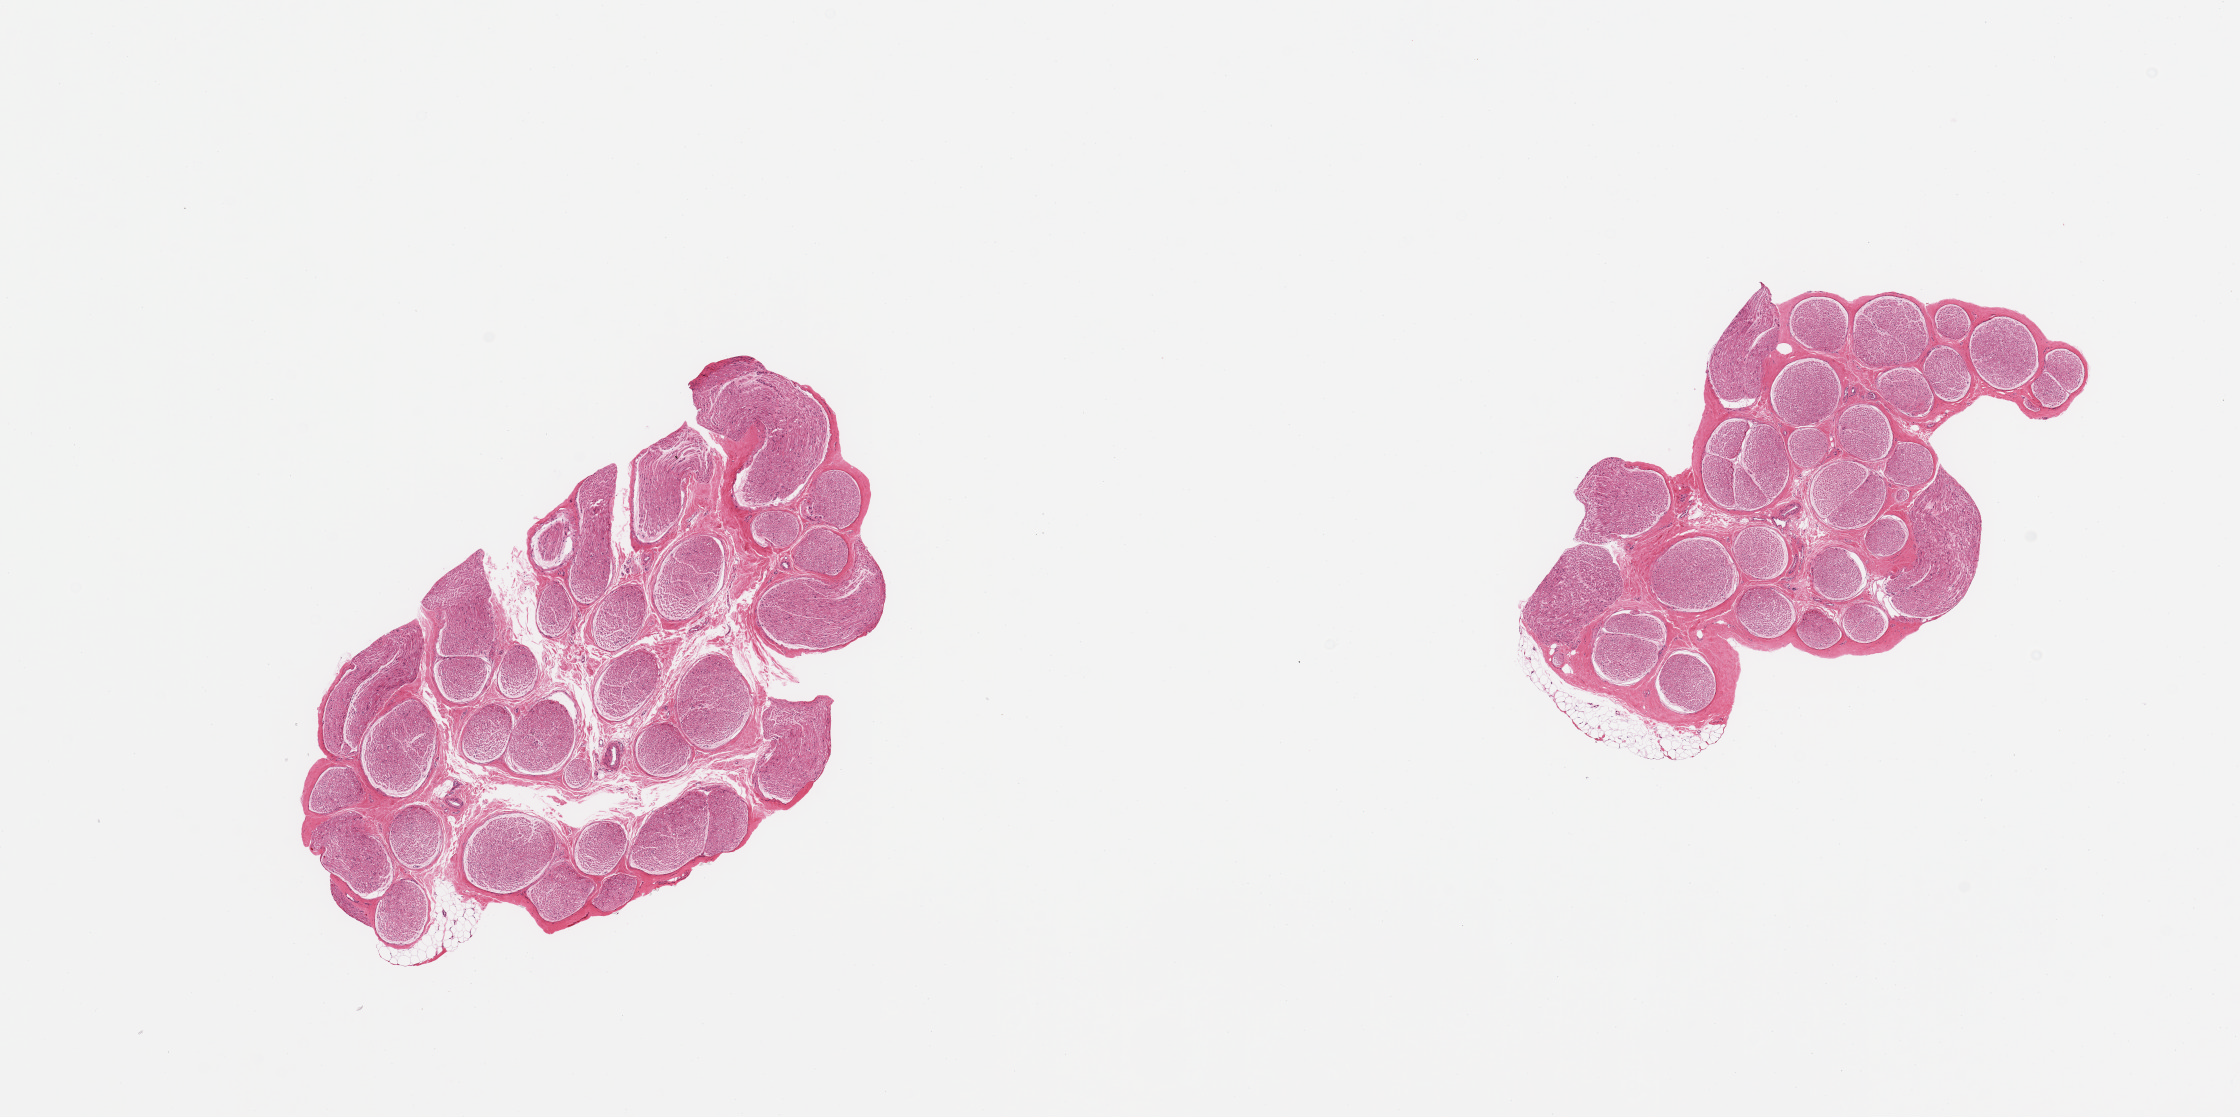
Digitized haematoxylin and eosin-stained section — whole scanned area (about 17.7 x 8.8 mm) shown as a low-resolution overview; PAXgene-fixed, paraffin-embedded tissue; section of tibial nerve (target tissue); donor tissue sample. Female donor.
Reviewer comment on this tissue sample: 2 pieces, minimal nubbin of adherent fat (~0.3mm).